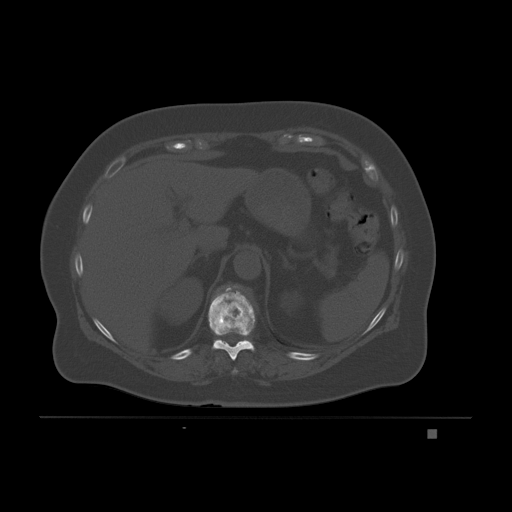
CT including the spine, one axial slice; position 98 of 221 along the scan axis; bone window (W 1800 / L 400 HU); 512 × 512 image matrix, field of view 474 × 474 mm. Female patient, age 63 years. Case-level facts recorded for this patient, not image findings: primary cancer: breast.
Structures marked on this image (semi-automatically segmented with operator editing):
- T10 vertebra: bounding box <208,289,255,360> (left, top, right, bottom; pixels)
- T11 vertebra: <227,285,238,289>
- T9 vertebra: <233,368,238,374>